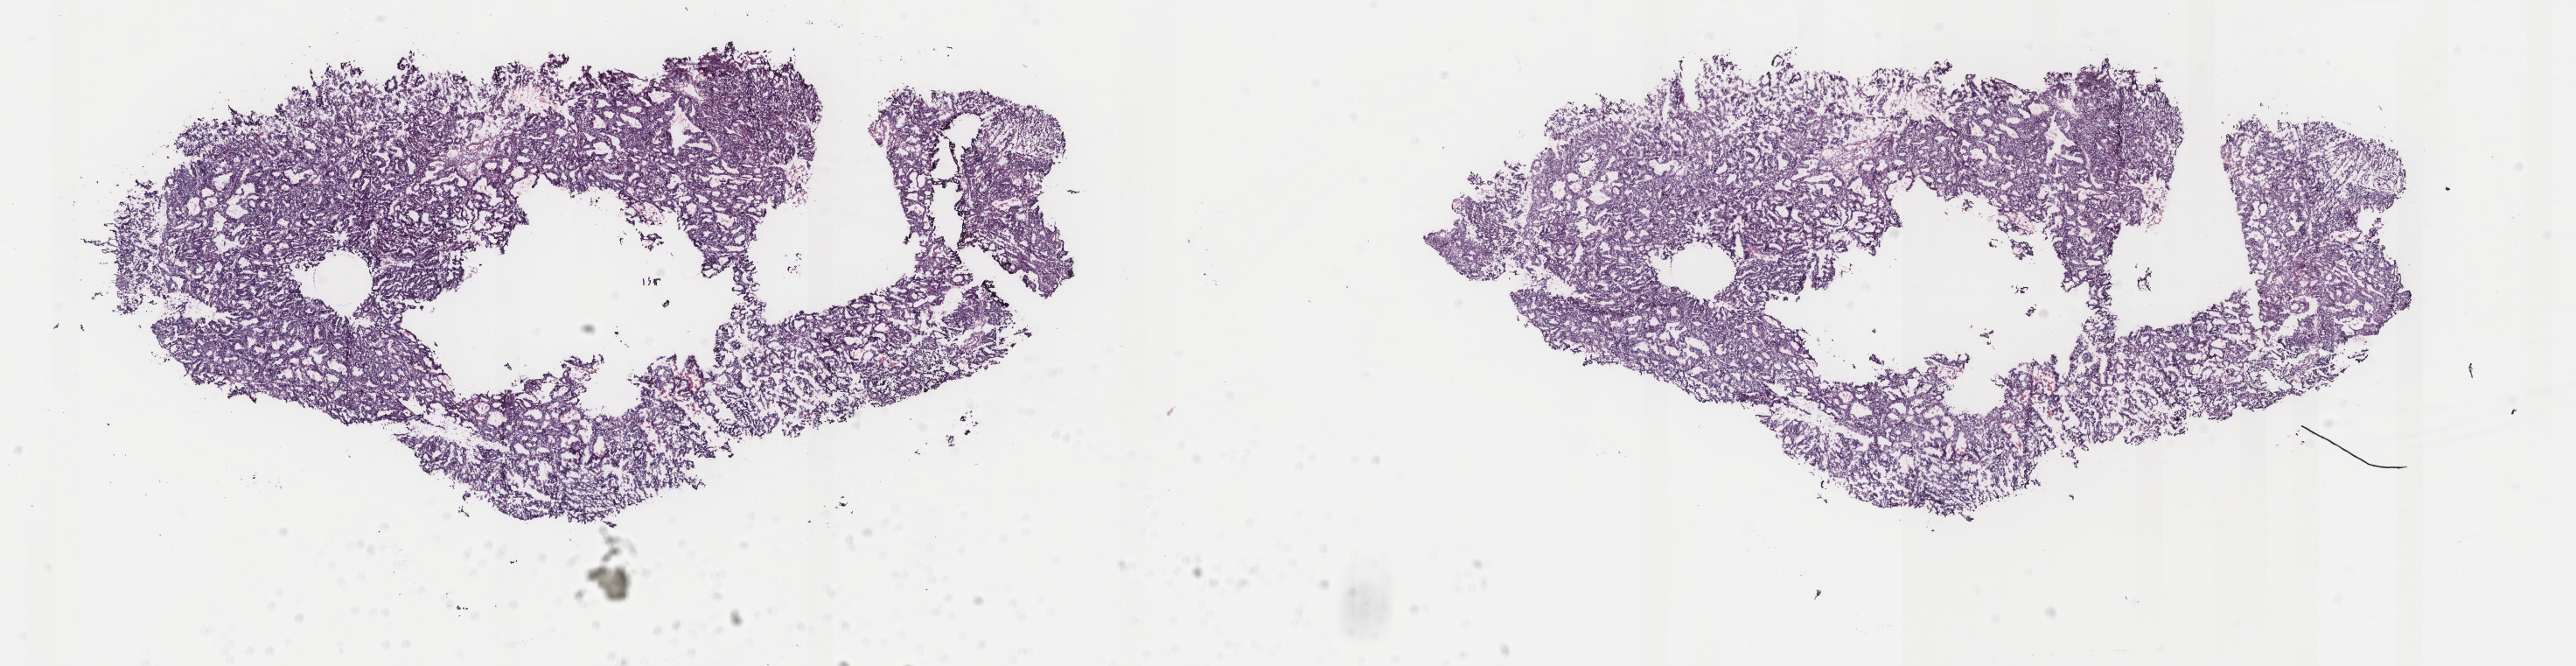
H&E whole-slide image — shown as a low-resolution overview of the whole scanned area (about 23.4 x 6.0 mm). Frozen section. Sample: primary tumour, uterus. Female, age 66 years at initial diagnosis. Histologic grade: G3 (poorly differentiated). Composition of this section per pathologist review: tumour cells 96%, tumour nuclei 95%, normal cells 0%, stromal cells 2%, necrosis 2%. Infiltration values recorded for this section: lymphocyte infiltration 2%, monocyte infiltration 1%, neutrophil infiltration 0%.
* FIGO stage: IB
* lymph nodes positive (case pathology): 0 of 12 examined
* histologic diagnosis: Endometrioid adenocarcinoma, NOS